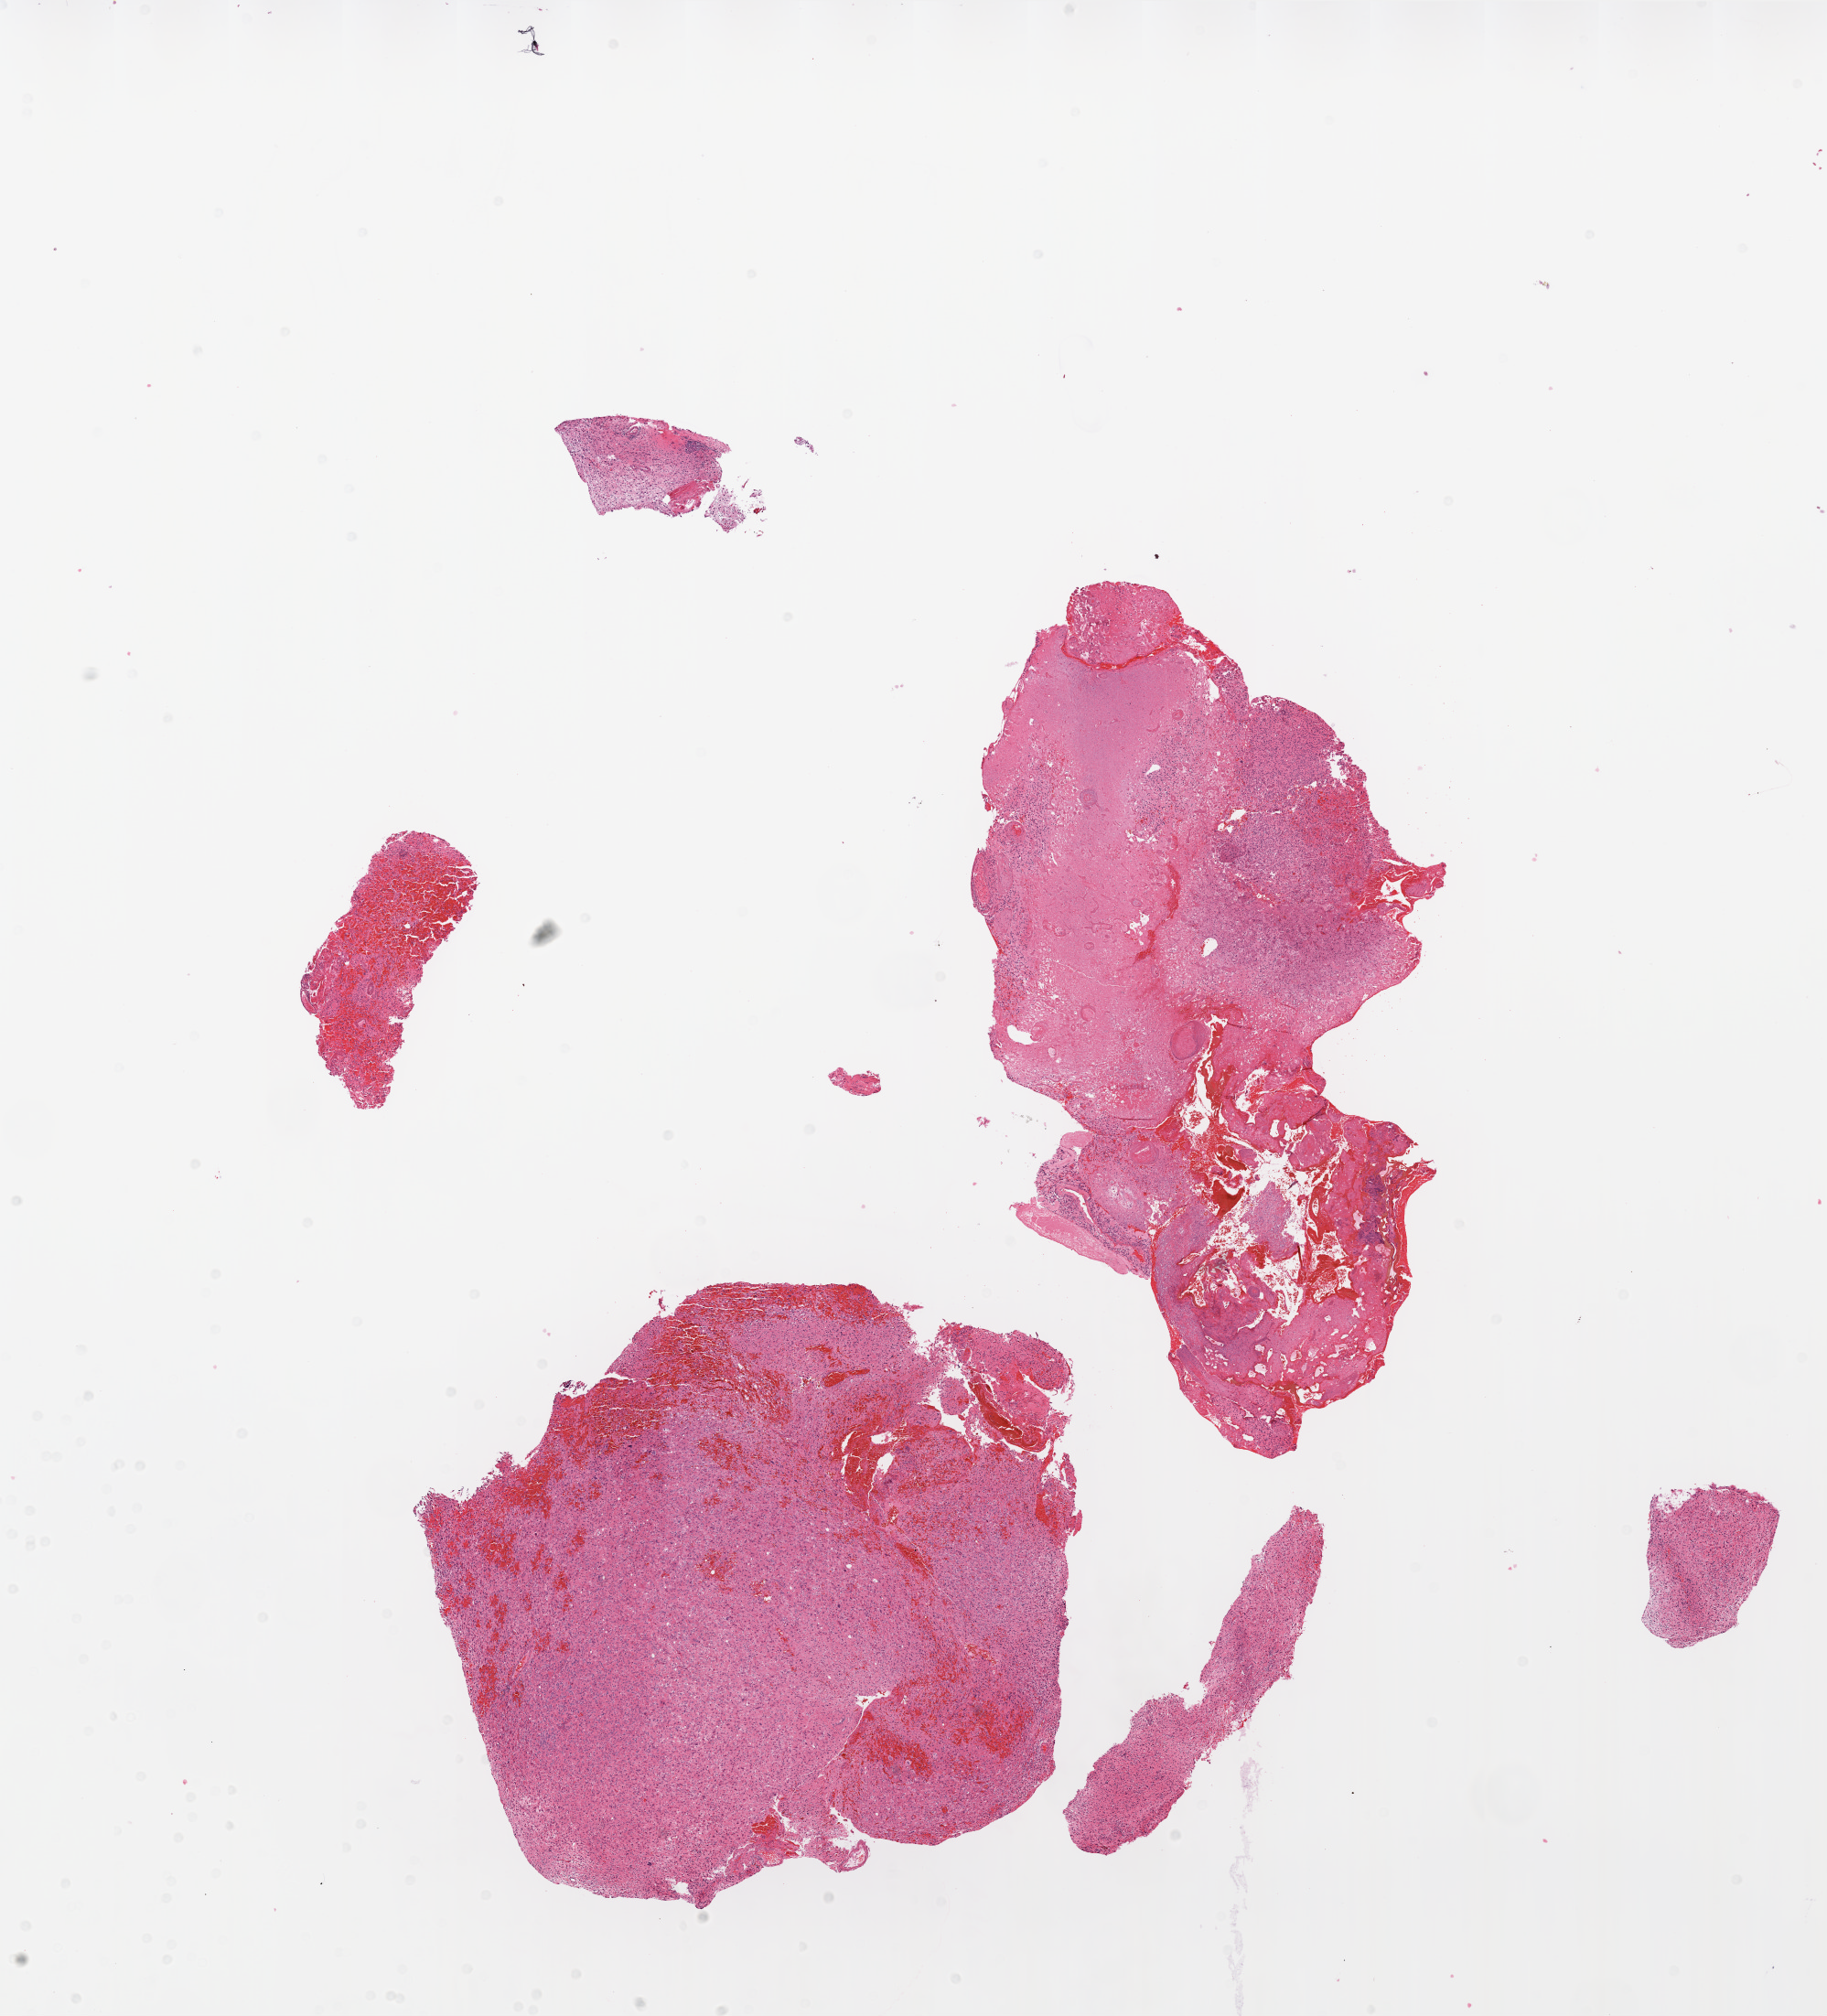
Digitized H&E-stained tissue section (whole slide) — shown as a low-resolution overview of the whole scanned area (about 16.0 x 17.6 mm, from a 20x scan), formalin-fixed paraffin-embedded (FFPE) diagnostic section, sample: primary tumour, brain. Male, age 76 years at initial diagnosis.
Pathologic diagnosis: Glioblastoma.